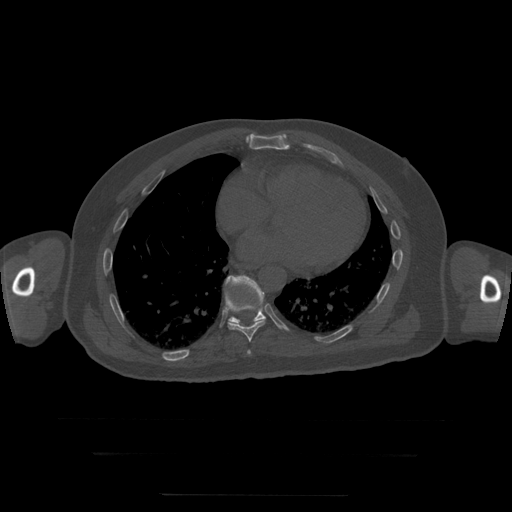
CT including the spine, one axial slice; slice 138 of 397 in the series (ordered by position); reconstruction kernel STANDARD; 120 kVp; bone window (W 1800 / L 400 HU); 1.25 mm slice thickness; 512 × 512 image matrix, field of view 510 × 510 mm. Patient age 73 years. Case-level facts recorded for this patient, not image findings: primary cancer: prostate.
Annotated regions visible in this slice (semi-automatic segmentation, software-assisted and operator-edited):
- T10 vertebra: bounding box [x1, y1, x2, y2] px = [226, 276, 266, 324]
- T8 vertebra: [247, 351, 251, 355]
- T9 vertebra: [224, 293, 266, 342]